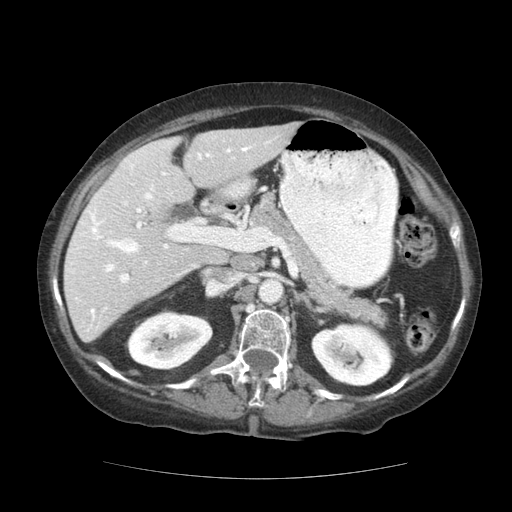
Contrast-enhanced abdominal CT (liver protocol), one axial slice; position 69 of 111 along the scan axis; 140 kVp; soft-tissue window (W 400 / L 40 HU); 512 × 512 image matrix, field of view 360 × 360 mm. From the clinical record (not read from this slice): diagnosis: hepatocellular carcinoma (patient treated with transarterial chemoembolisation; whether this scan precedes or follows treatment is not stated here); TNM stage (as recorded): Stage-I; Child-Pugh class: A; tumour differentiation: moderately-poorly differentiated; tumour size: 7.3 cm.
Annotated regions visible in this slice (semi-automatic segmentation, software-assisted and operator-edited):
- liver parenchyma outside the tumour (the mass and vessels are separate outlines, so this box may not span the whole liver): bounding box (x1, y1, x2, y2) in pixels: (64, 122, 298, 342)
- liver vessels: (68, 141, 272, 331)